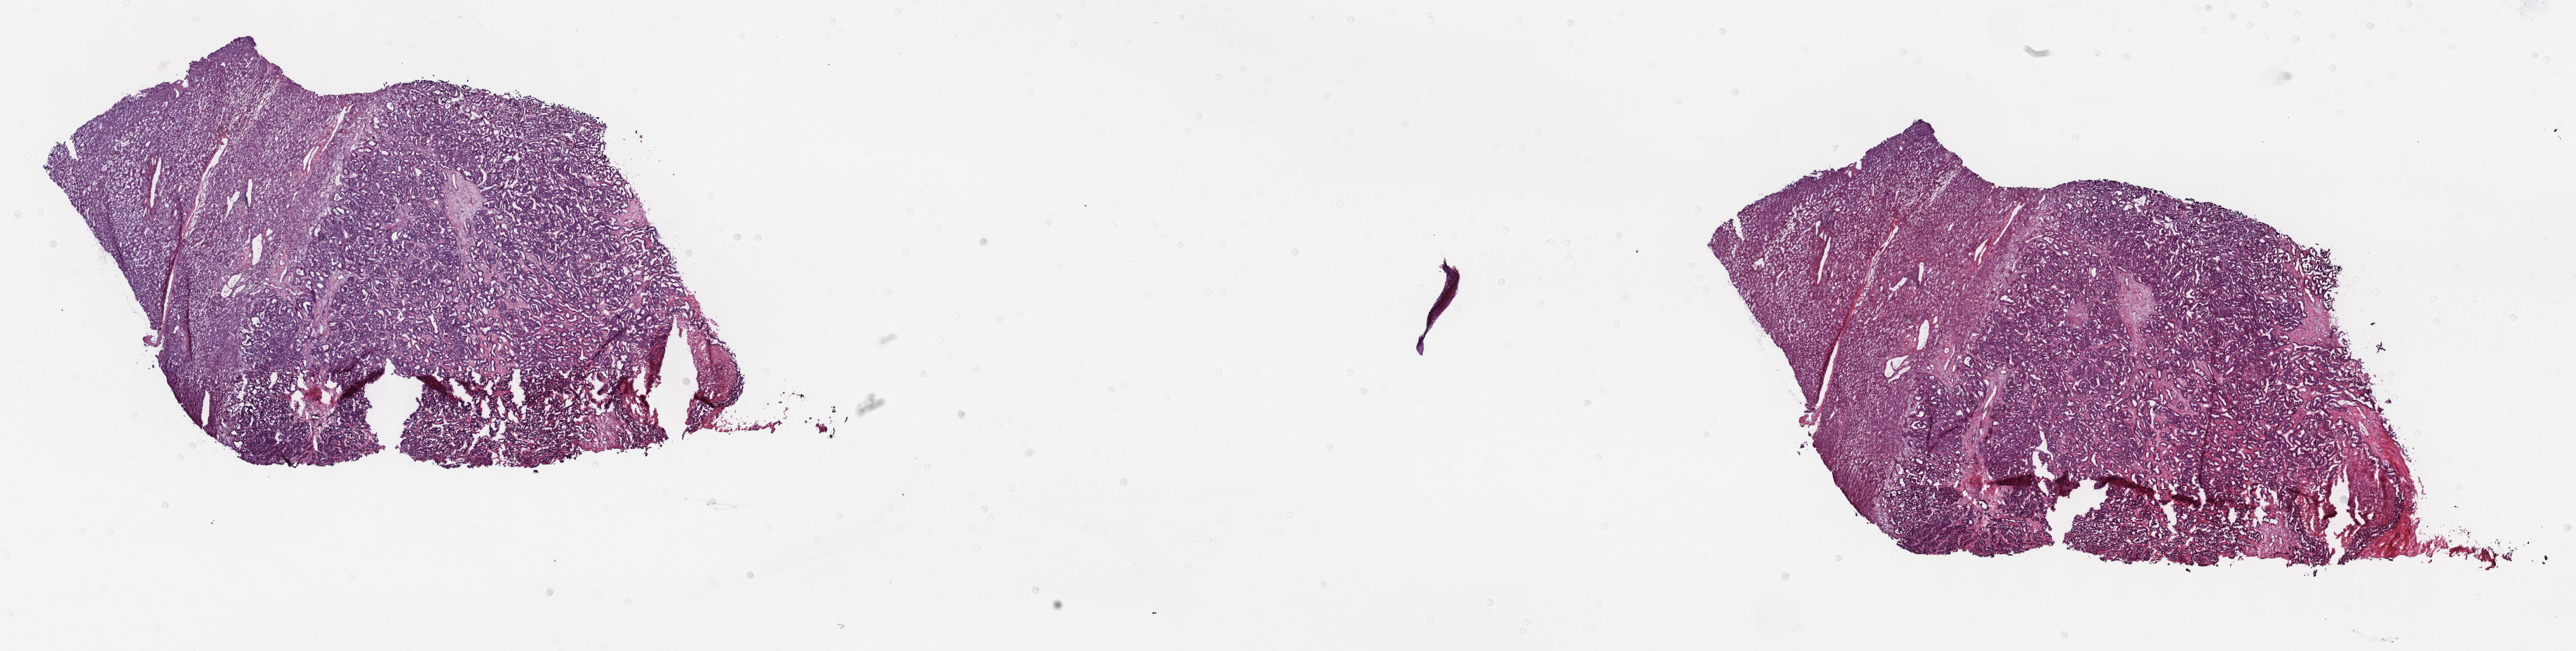
Whole-slide histology image, Hematoxylin and eosin (H&E) stained — whole scanned area (about 29.7 x 7.5 mm, from a 40x scan) shown as a low-resolution overview; frozen section; sample: primary tumour, bile duct. Female, age 64 years at initial diagnosis. Slide review estimates, as recorded: tumour cells 65%, tumour nuclei 60%.
Pathologic diagnosis: Cholangiocarcinoma.